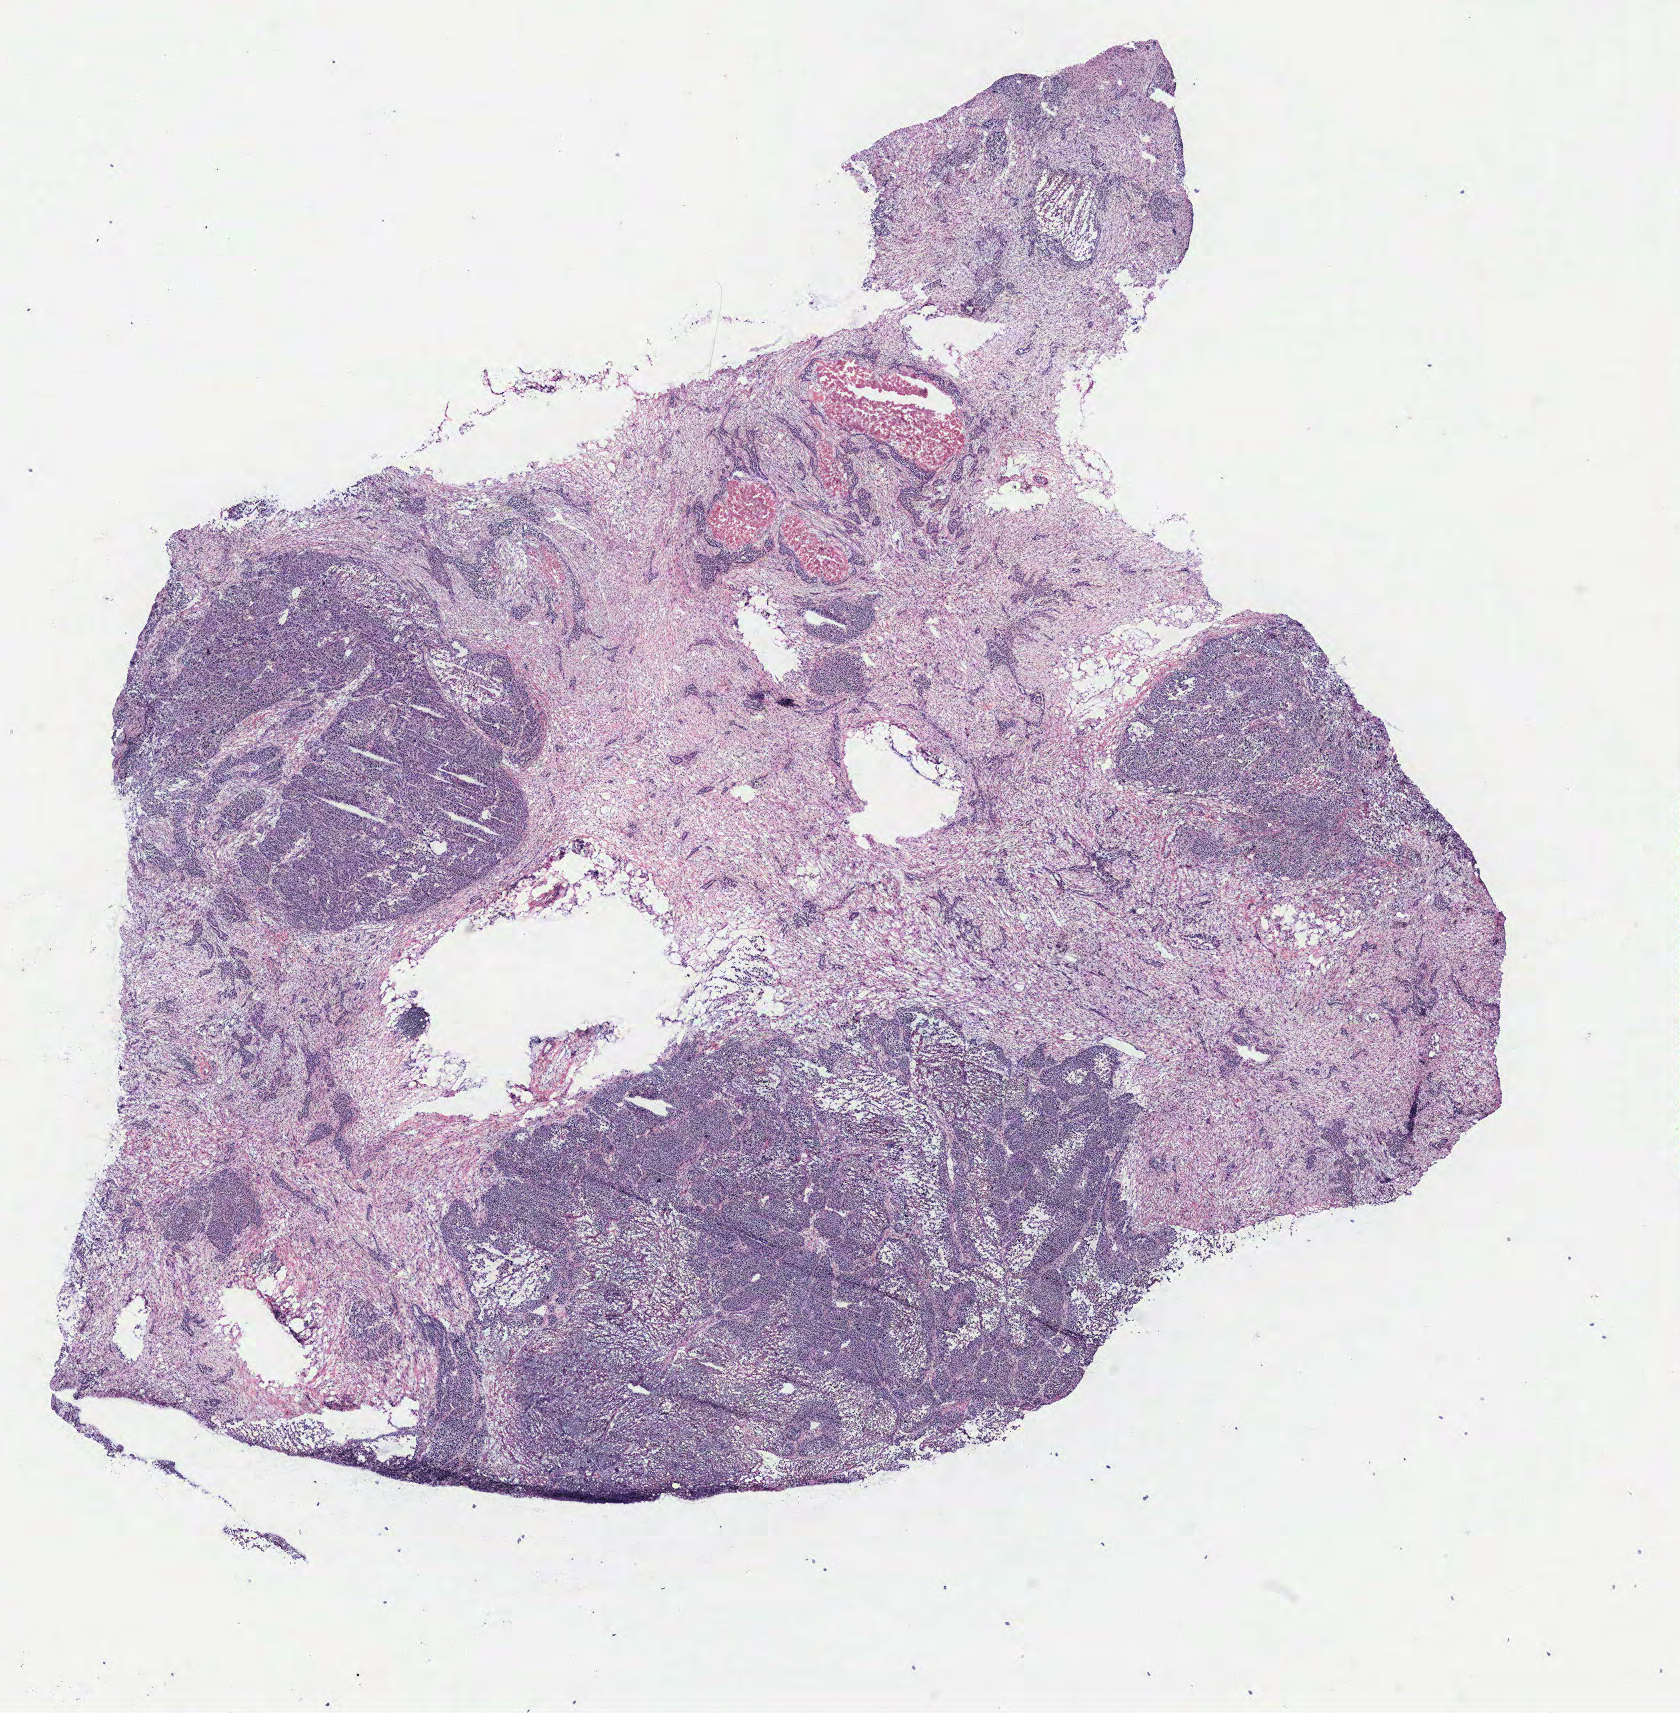
Whole-slide histology image, H&E-stained, shown as a low-resolution overview of the whole scanned area (about 13.4 x 13.7 mm, acquisition: 40x scan); ovary, tissue type not recorded. Female patient.
* patient diagnosis: Serous adenocarcinoma, NOS